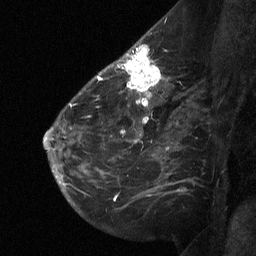
Breast MRI (dynamic contrast-enhanced), one sagittal slice; slice 40 of 64 in the series (ordered by position); dynamic contrast-enhanced study with each time point stored as its own series, time point 2 of 3 at this slice position (early post-contrast, ordered by acquisition time); 1.5 T; TE 4.8 ms, TR 27 ms; 2 mm slice thickness; 256 × 256 image matrix, field of view 200 × 200 mm. Patient: female, 51 years. From the clinical record (not read from this slice): setting: breast cancer imaged before/during neoadjuvant chemotherapy; receptor status: HR-positive, HER2-negative.
Annotated regions visible in this slice (semi-automatic segmentation, software-assisted and operator-edited):
- analysis volume of interest (the breast-tissue region the enhancement analysis was run in; not a lesion): bounding box (x1, y1, x2, y2) in pixels: (112, 46, 169, 106)
- tumour enhancement mask (voxels above the 90 % enhancement threshold inside the analysis volume of interest): (122, 46, 162, 106)